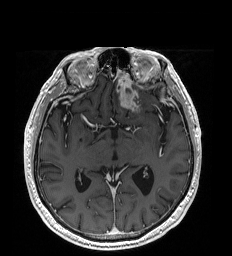
Brain MRI from a brain-tumour surgery series, one axial slice. Slice 110 of 192 in the series (ordered by position). T1-weighted post-contrast. 1 mm slice thickness. 232 × 256 image matrix, field of view 227 × 250 mm. Case-level facts recorded for this patient, not image findings: histopathology: Glioblastoma; WHO grade: 4; IDH mutation: no.
Annotated regions visible in this slice (outlined manually by an expert reader):
- tumour: bounding box <118,87,138,111> (left, top, right, bottom; pixels)